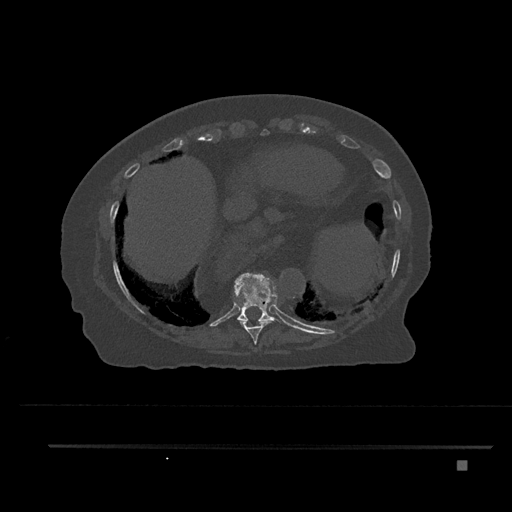
CT including the spine, one axial slice. Slice 377 of 797 in the series (ordered by position). Reconstruction kernel Br40s/3. 120 kVp. Bone window (W 1800 / L 400 HU). 512 × 512 image matrix, field of view 437 × 437 mm. Female patient, age 76 years. From the clinical record (not read from this slice): primary cancer: lung; vertebrae with lytic lesions (as recorded): T11, L3.
Outlined on this slice (semi-automatic segmentation, software-assisted and operator-edited):
- T10 vertebra: bounding box <234,273,286,324> (left, top, right, bottom; pixels)
- T9 vertebra: <234,287,271,344>